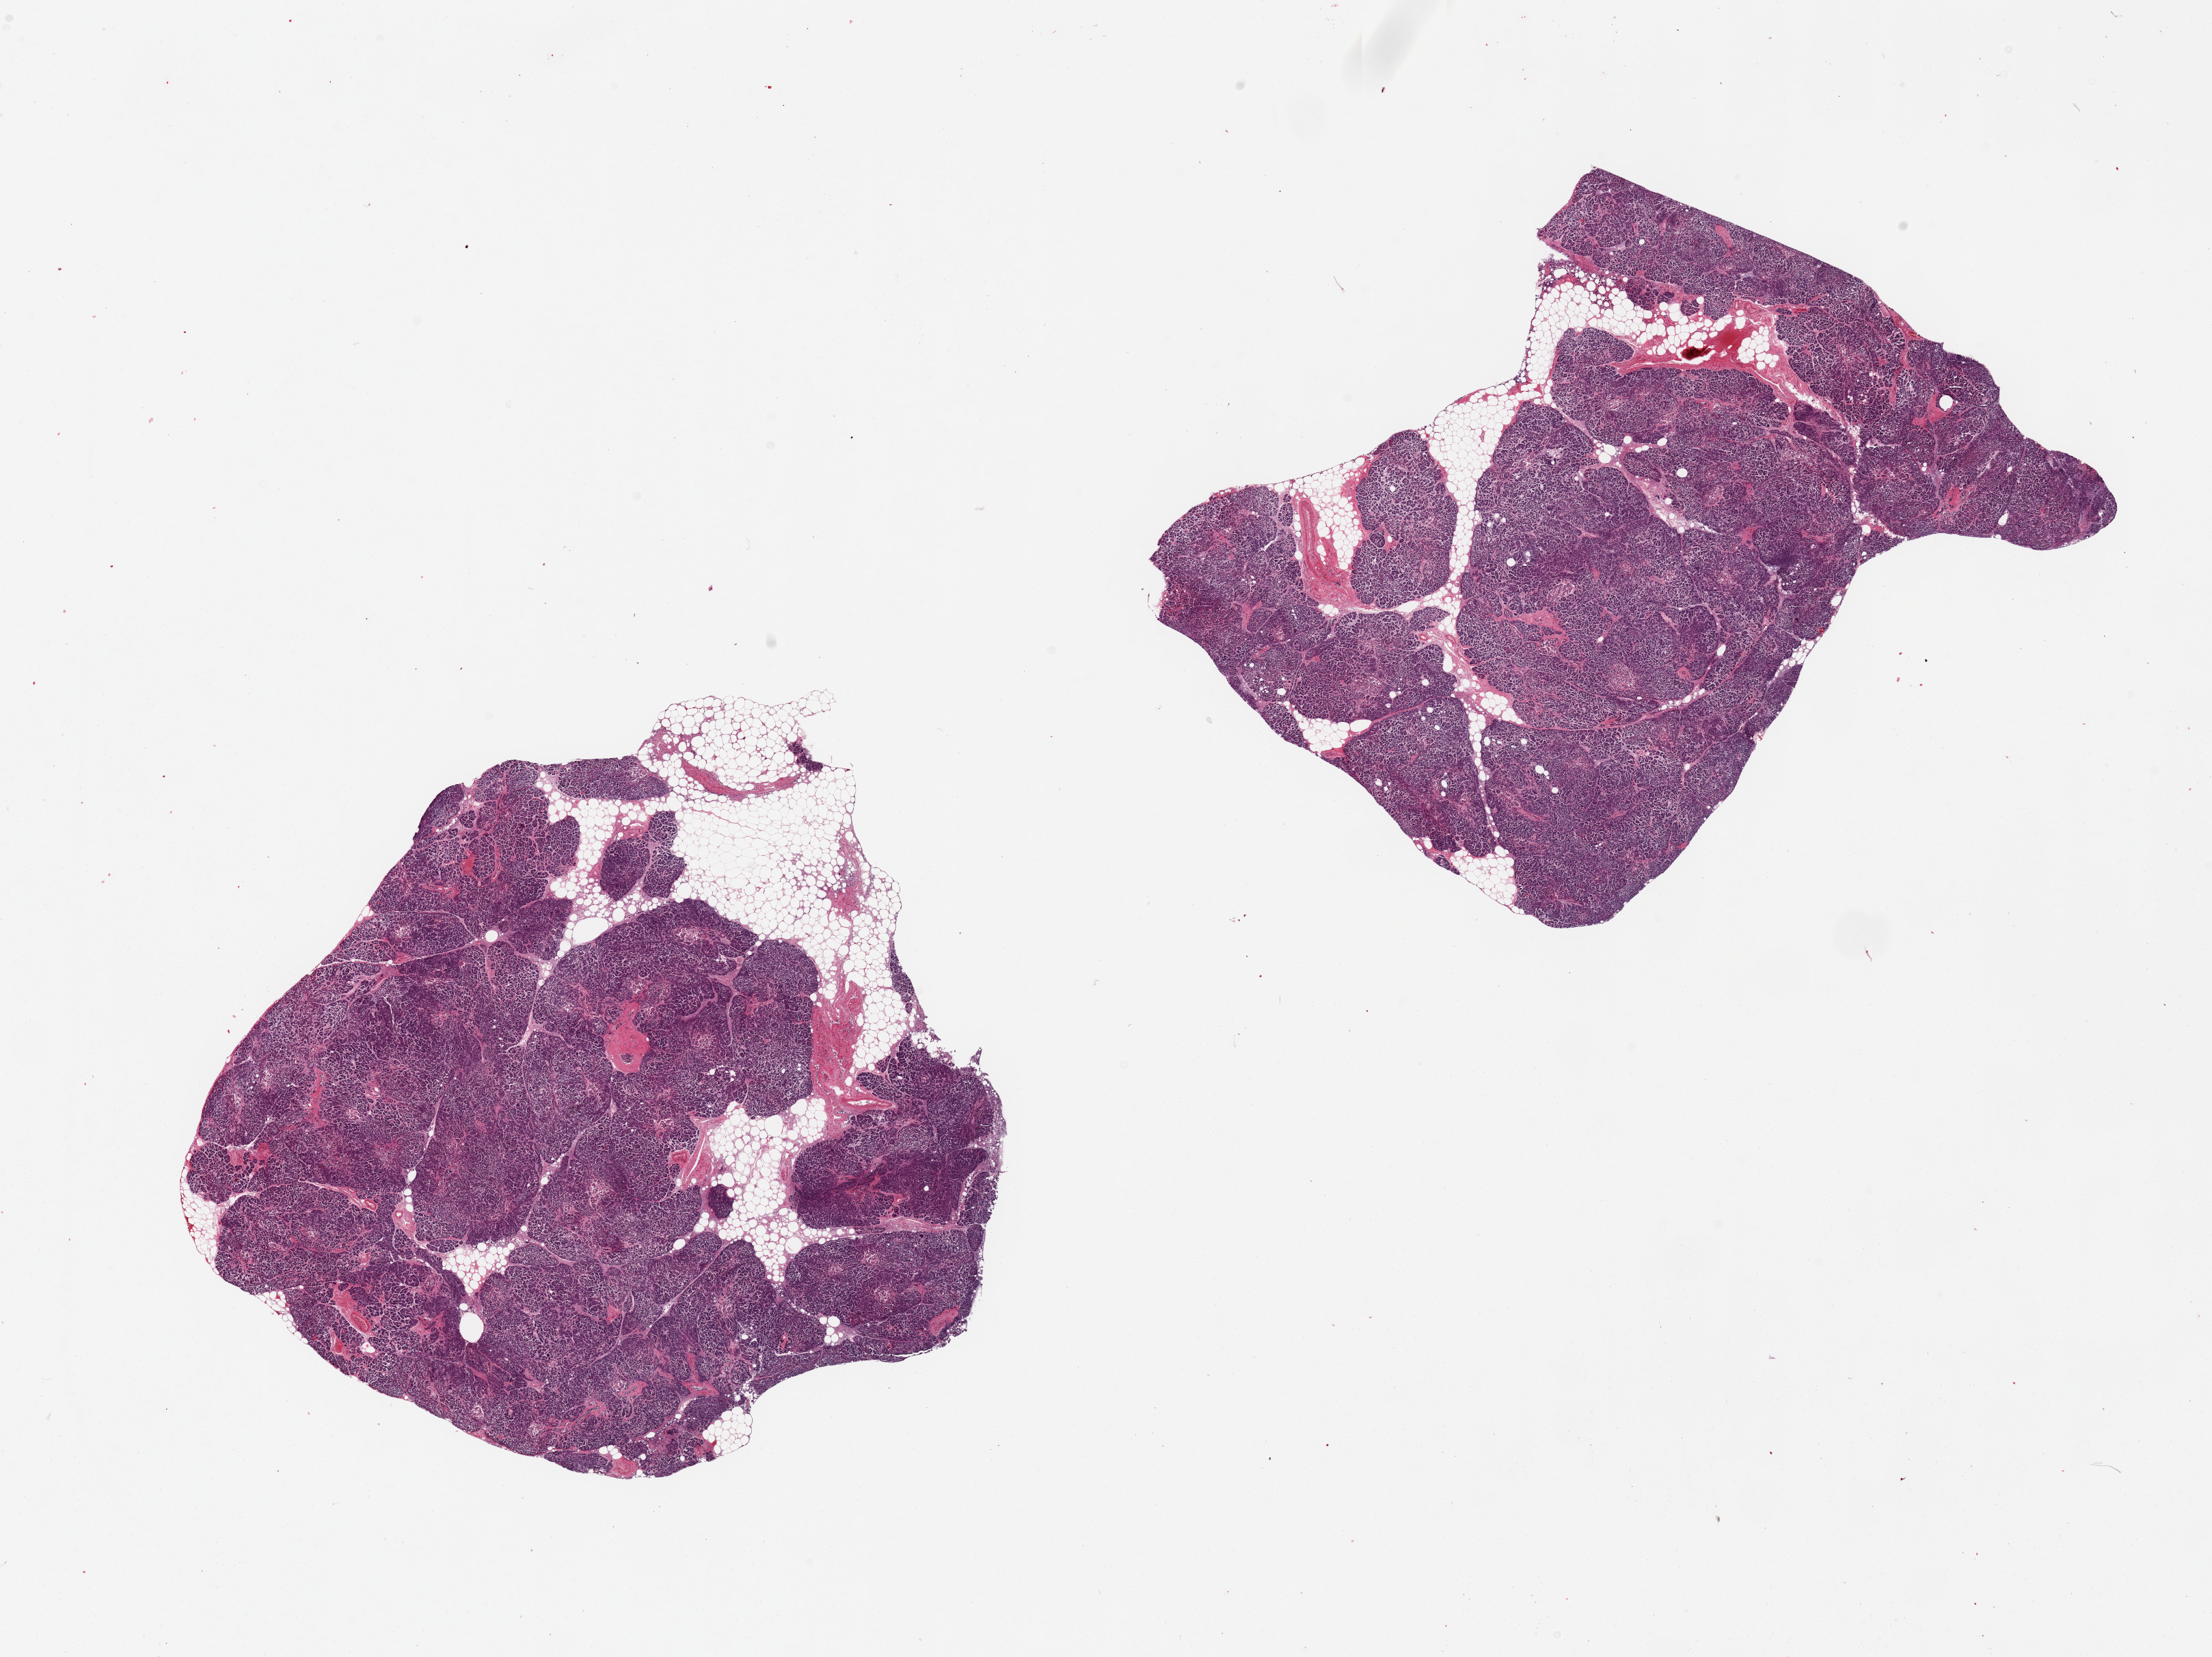
Whole-slide image, H&E stain, shown as a low-resolution overview of the whole scanned area (about 25.6 x 19.2 mm, slide scanned at 20x), PAXgene-fixed, paraffin-embedded tissue, target tissue: pancreas, tissue donor sample. Male donor.
* pathologist's review note for this sample: 2 pieces, 9.5x8 and 8x7mm; moderate to focally marked saponification